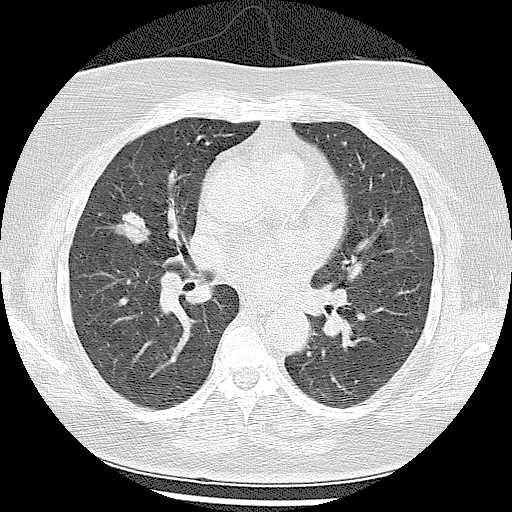
Low-dose screening chest CT, one axial slice. Position 52 of 102 along the scan axis. 120 kVp. Lung window (W 1500 / L -600 HU). 2.5 mm slice thickness. 512 × 512 image matrix.
Structures marked on this image (expert manual segmentation):
- lesion 1 (tumor, middle lobe of right lung): box from (x=112, y=211) to (x=151, y=244) px